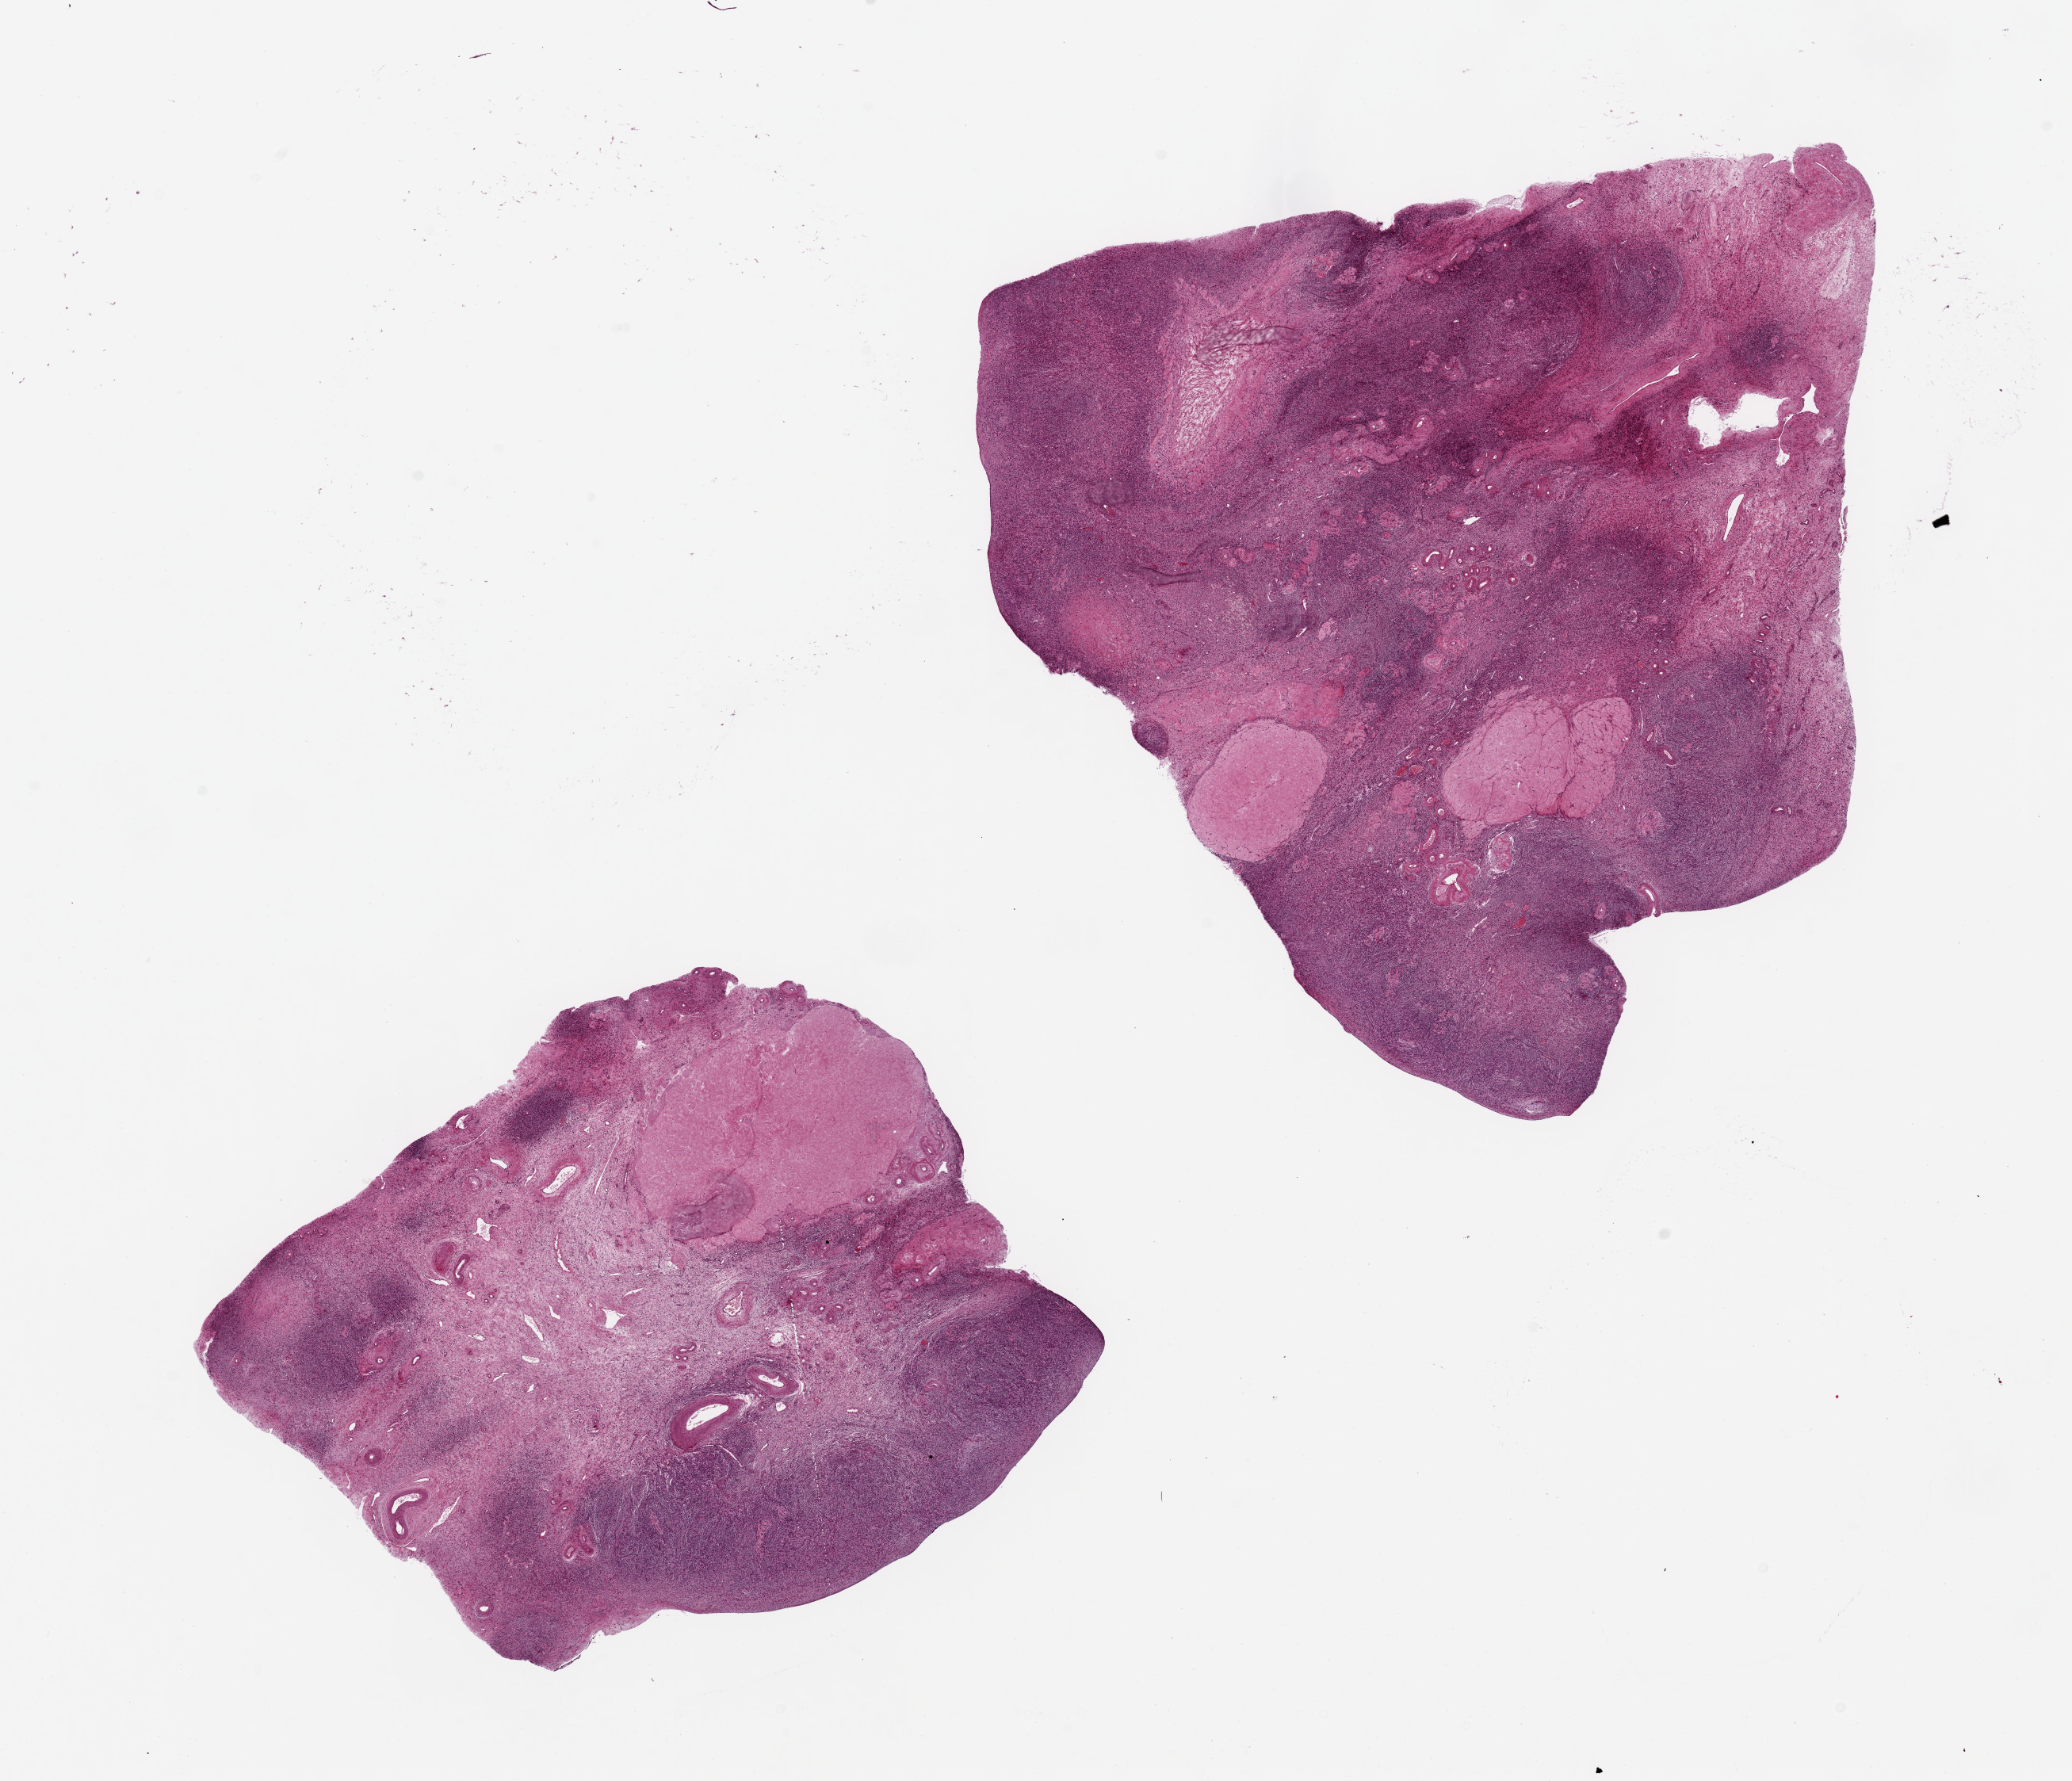
Whole-slide image, hematoxylin and eosin (H&E) stain — low-resolution overview of the scanned area, about 20.7 x 17.8 mm; PAXgene-fixed paraffin-embedded (PFPE) section; sampled site (target tissue): ovary; tissue donor sample. Female donor.
Pathologist's review note for this sample: 2 pieces, 8x6.5 & 10x10mm; corpora albicans; atrophic.